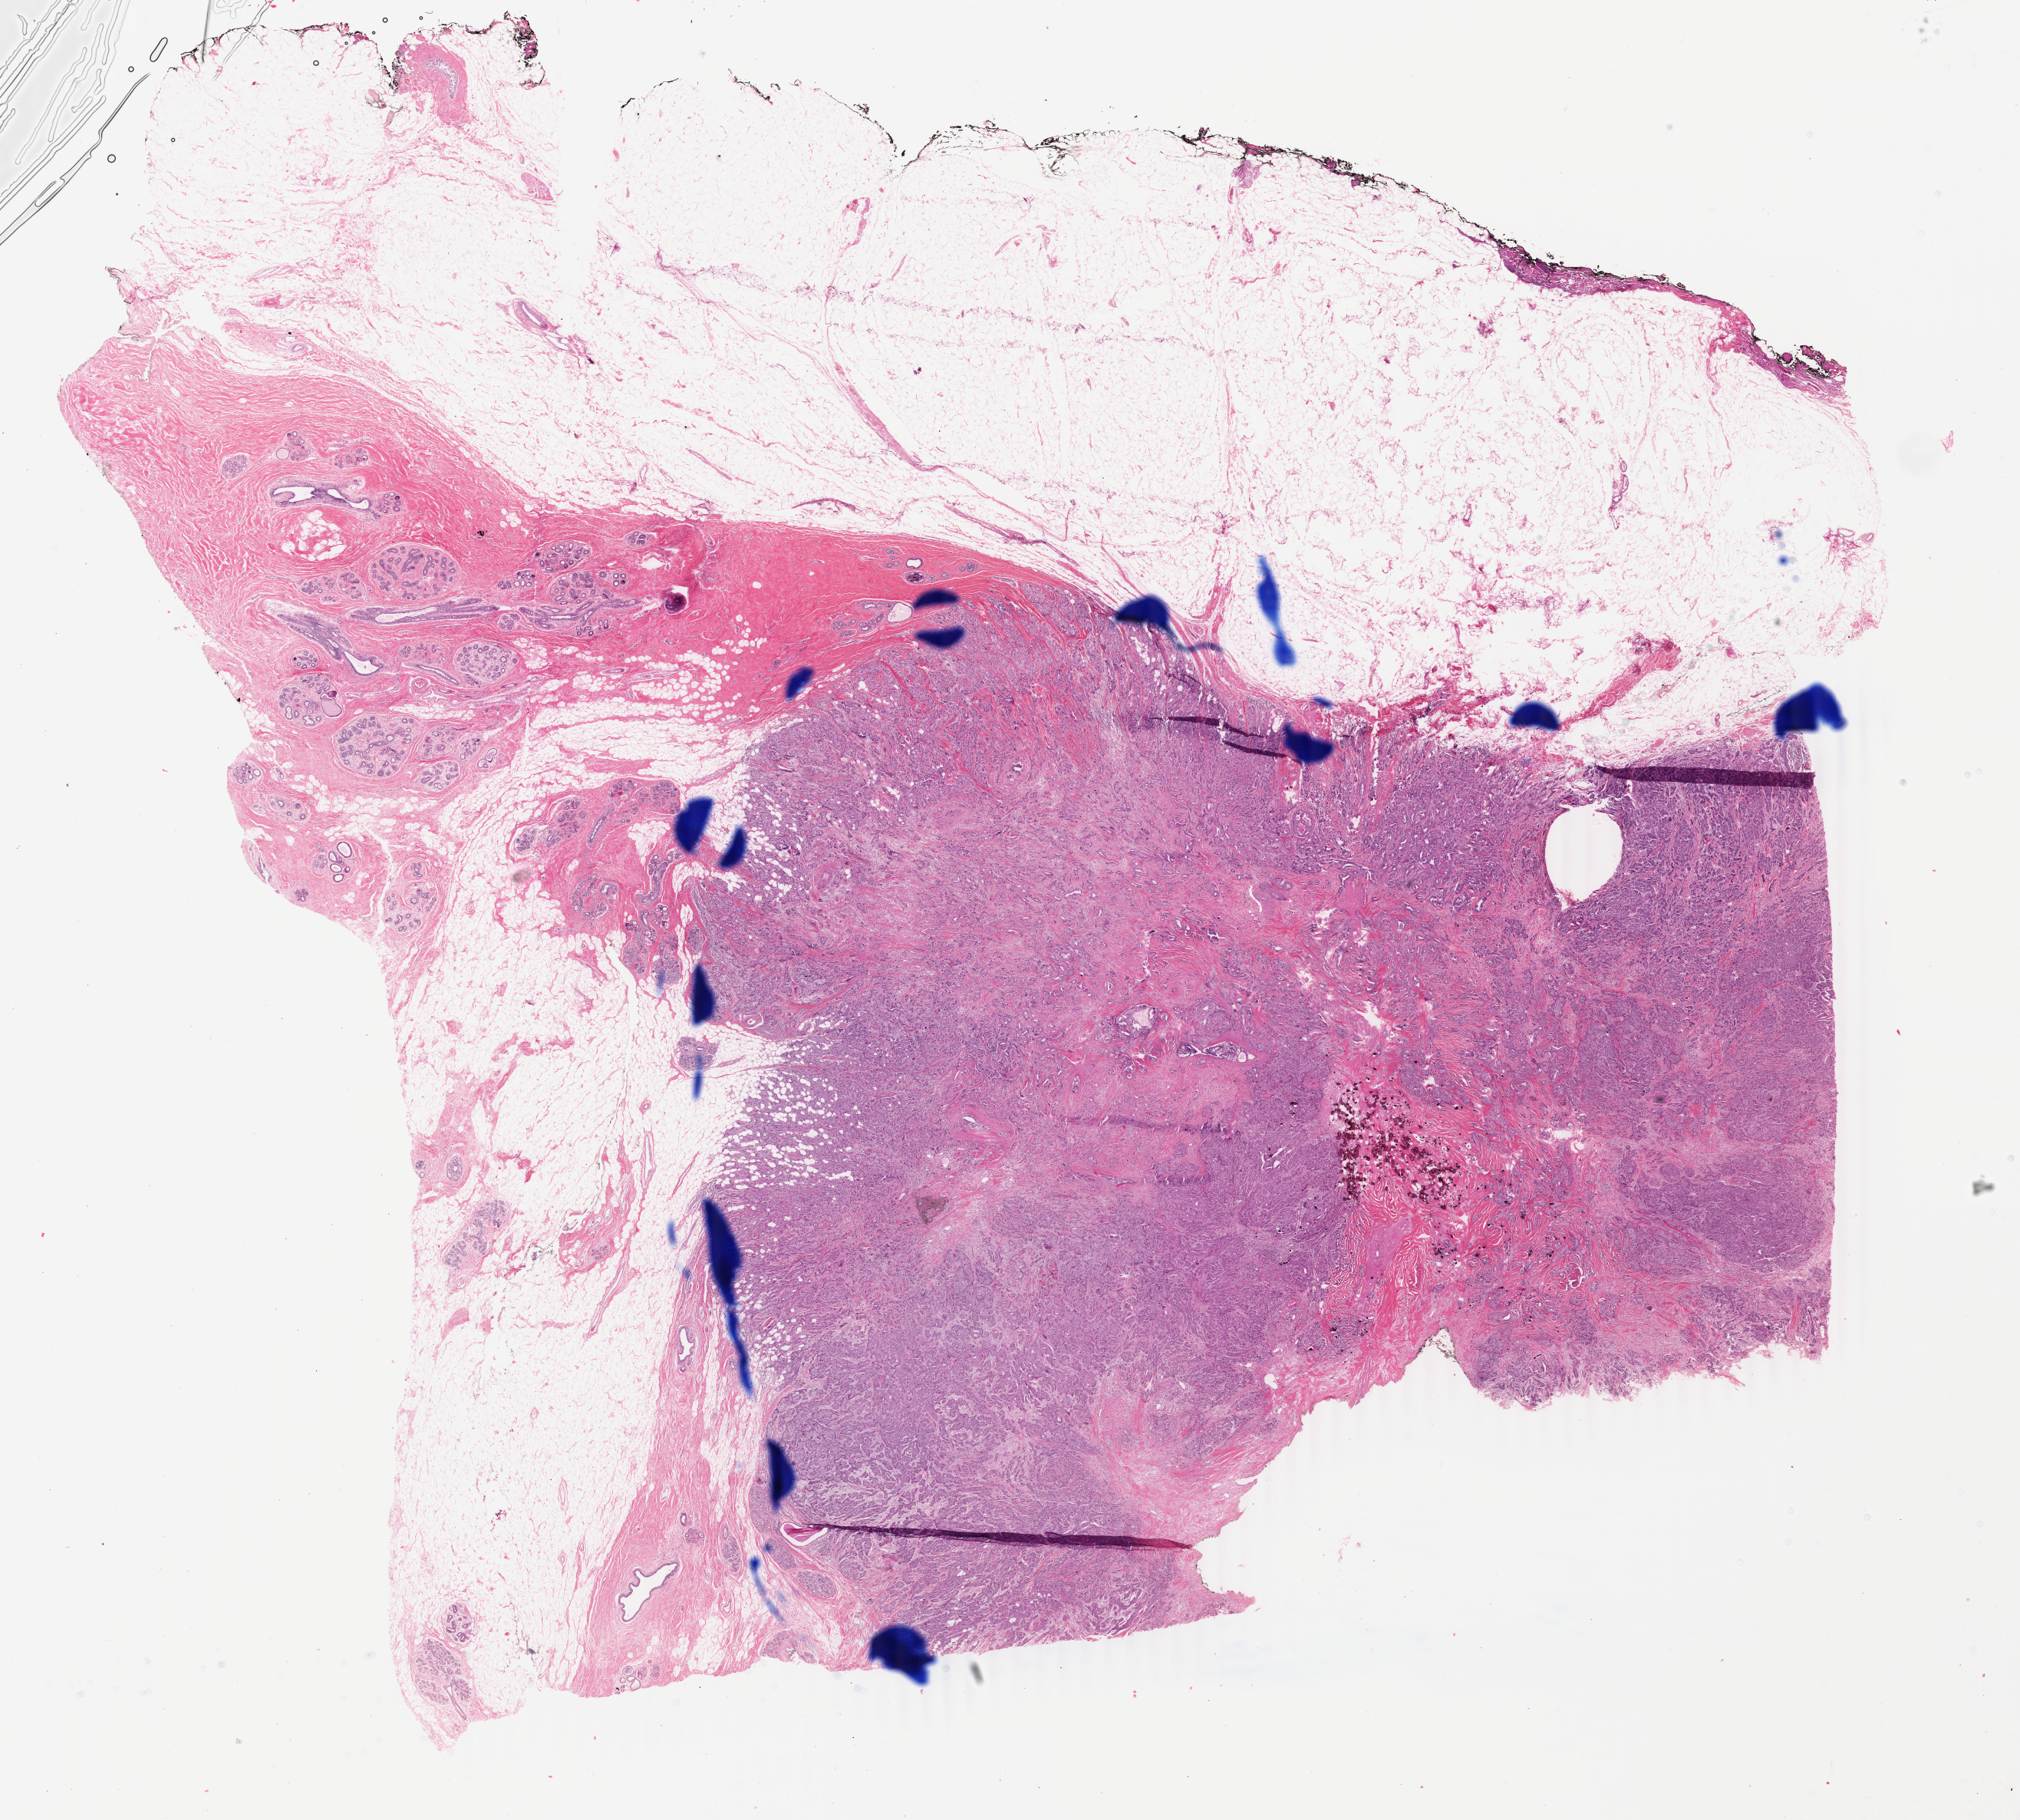
Whole-slide histology image, Hematoxylin and eosin (H&E) stained — shown as a low-resolution overview of the whole scanned area (about 20.9 x 18.9 mm, slide scanned at 40x), FFPE section, sample: primary tumour, breast. Female patient; age at initial diagnosis 45 years.
• AJCC pathologic stage: IA
• histologic diagnosis: Infiltrating duct carcinoma, NOS
• TNM: T1c N0 (i-) M0